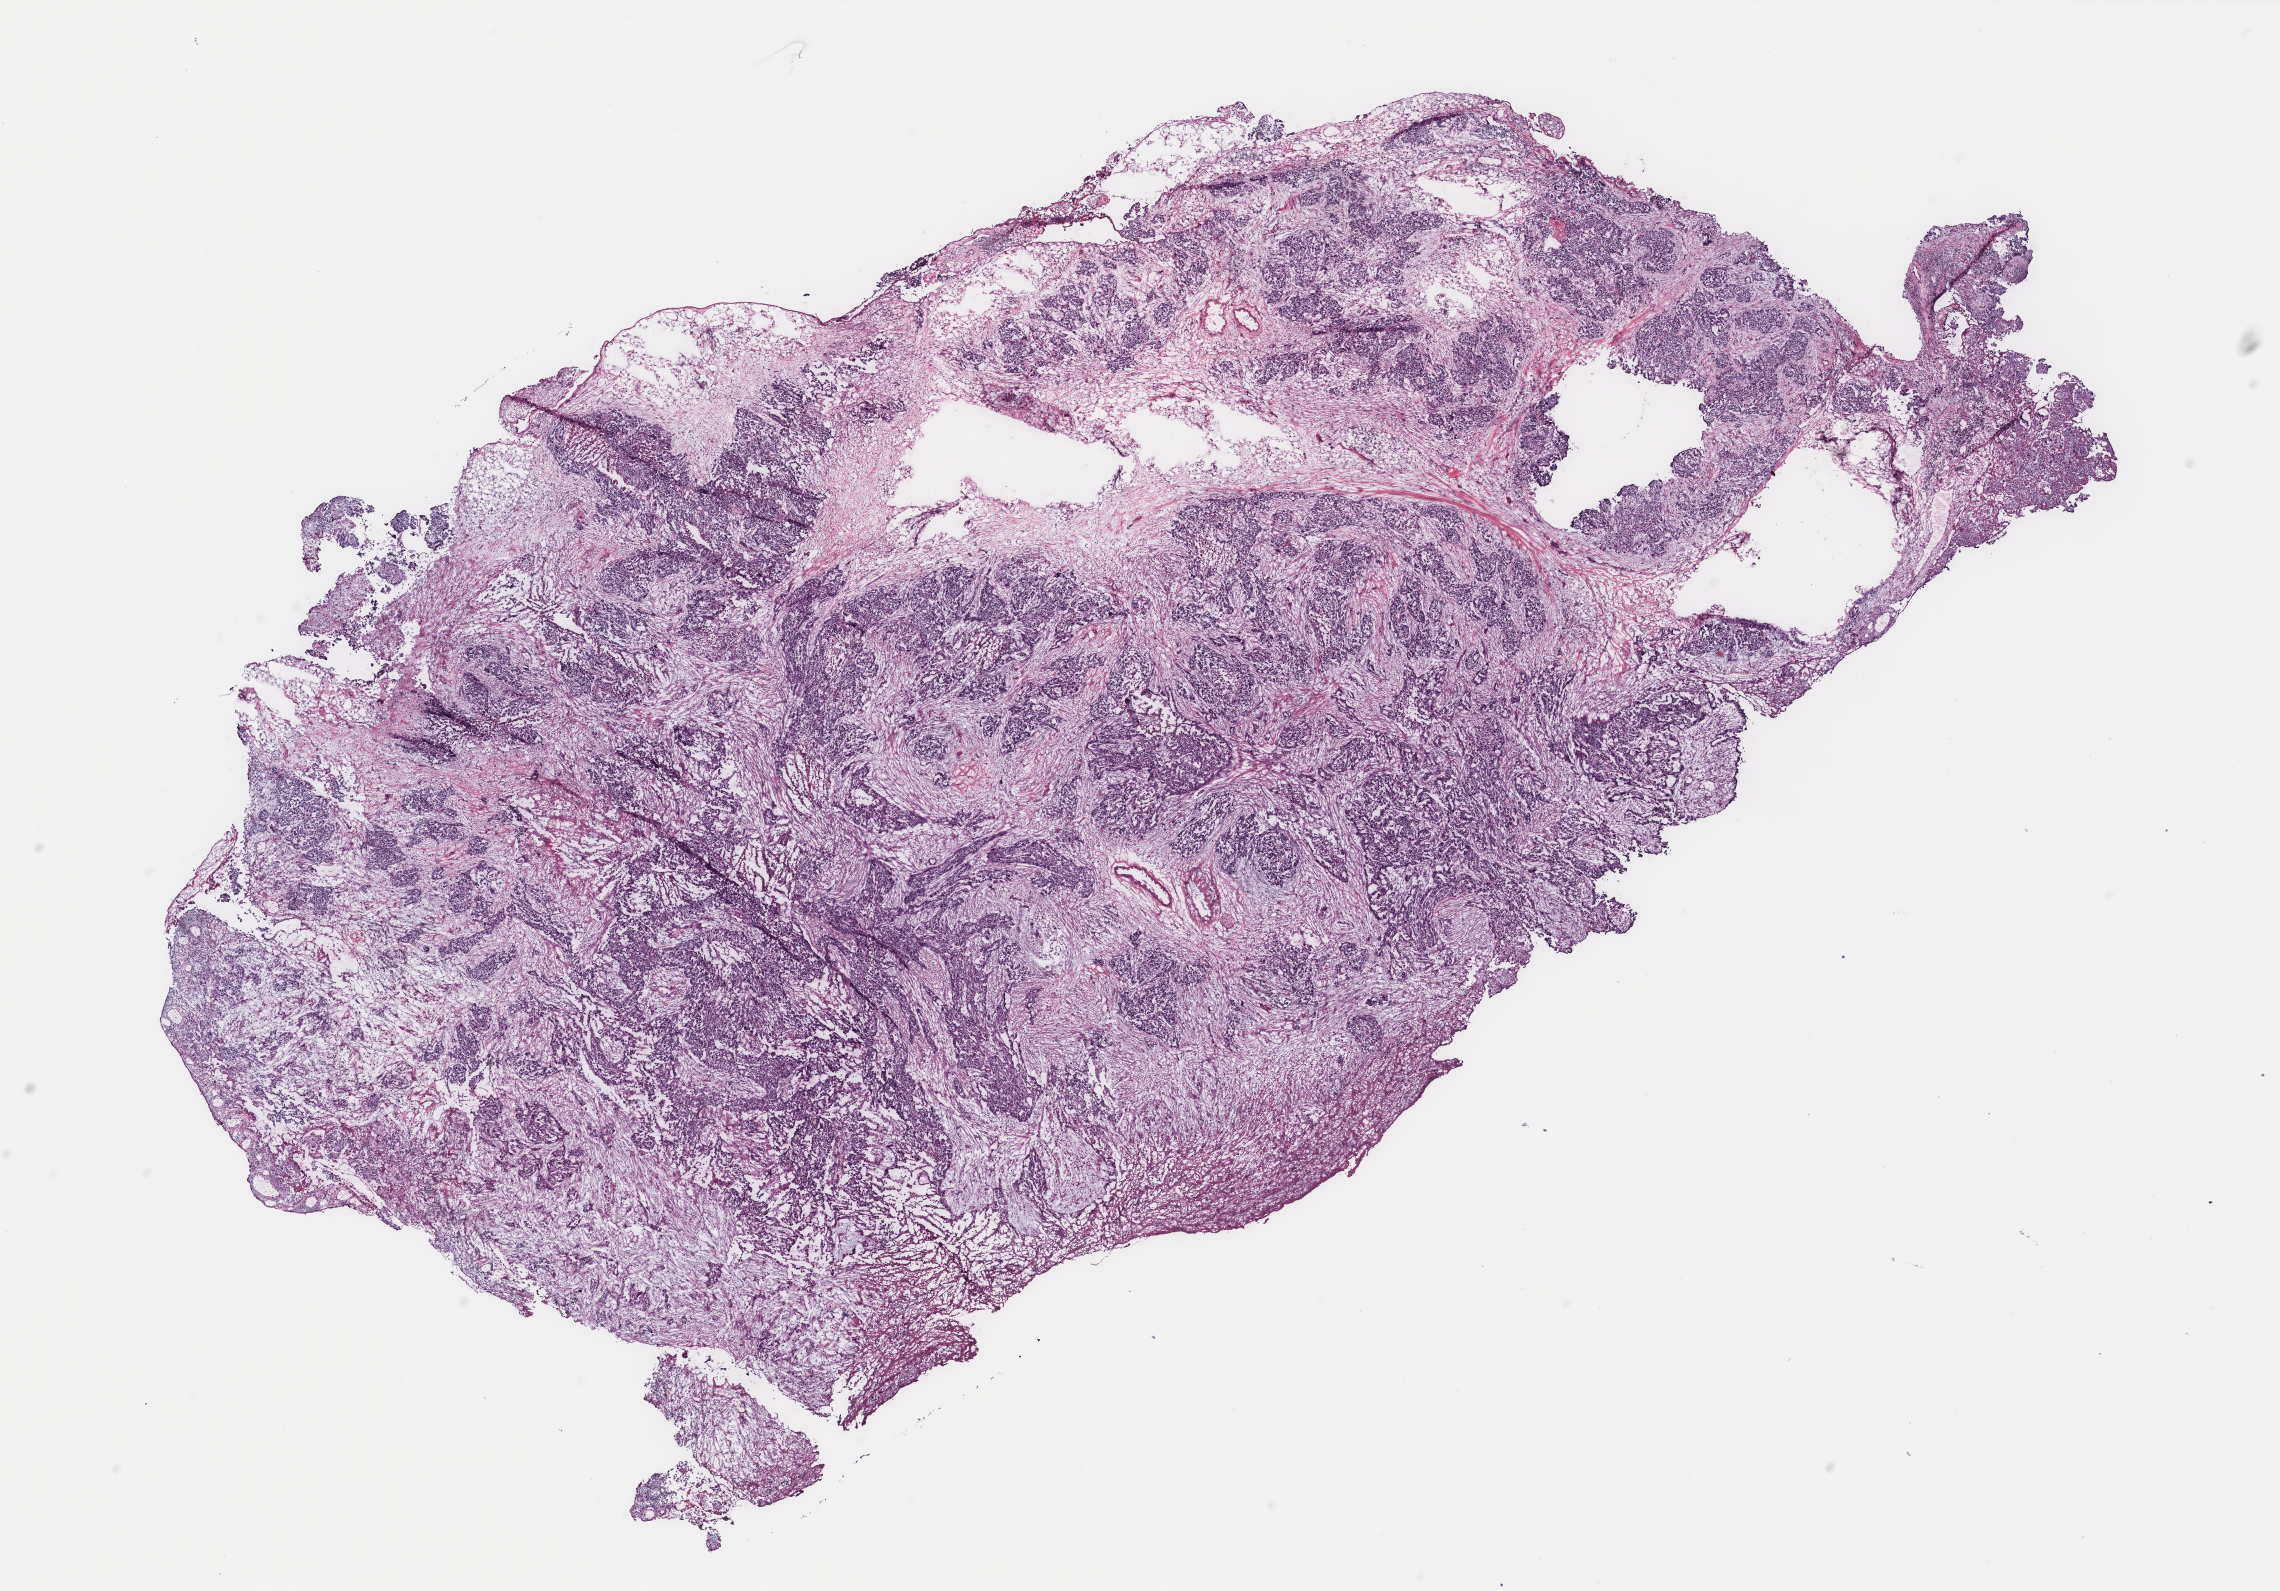
Hematoxylin and eosin (H&E) stained whole-slide image, a low-resolution overview of the entire scanned area, about 18.2 x 12.7 mm (slide scanned at 40x). Ovary, tissue type not recorded. Patient sex: female.
Patient diagnosis: Serous adenocarcinoma, NOS.